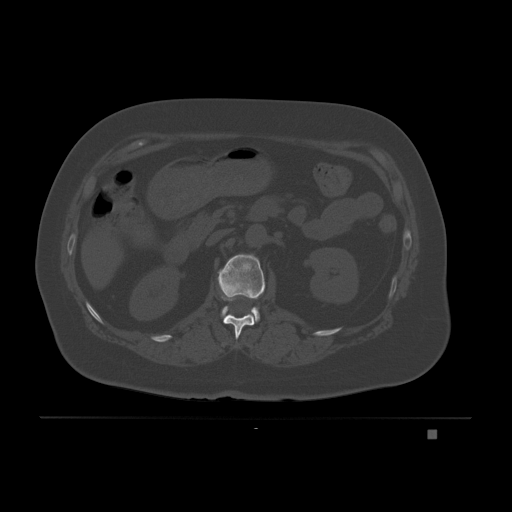
CT including the spine, one axial slice; position 76 of 221 along the scan axis; bone window (W 1800 / L 400 HU); 3 mm slice thickness; 512 × 512 image matrix, field of view 474 × 474 mm. Patient: female, 63 years. From the clinical record (not read from this slice): primary cancer: breast.
Outlined on this slice (semi-automatic segmentation, software-assisted and operator-edited):
- L1 vertebra: bounding box (x1, y1, x2, y2) in pixels: (218, 254, 266, 323)
- T12 vertebra: (223, 296, 255, 340)